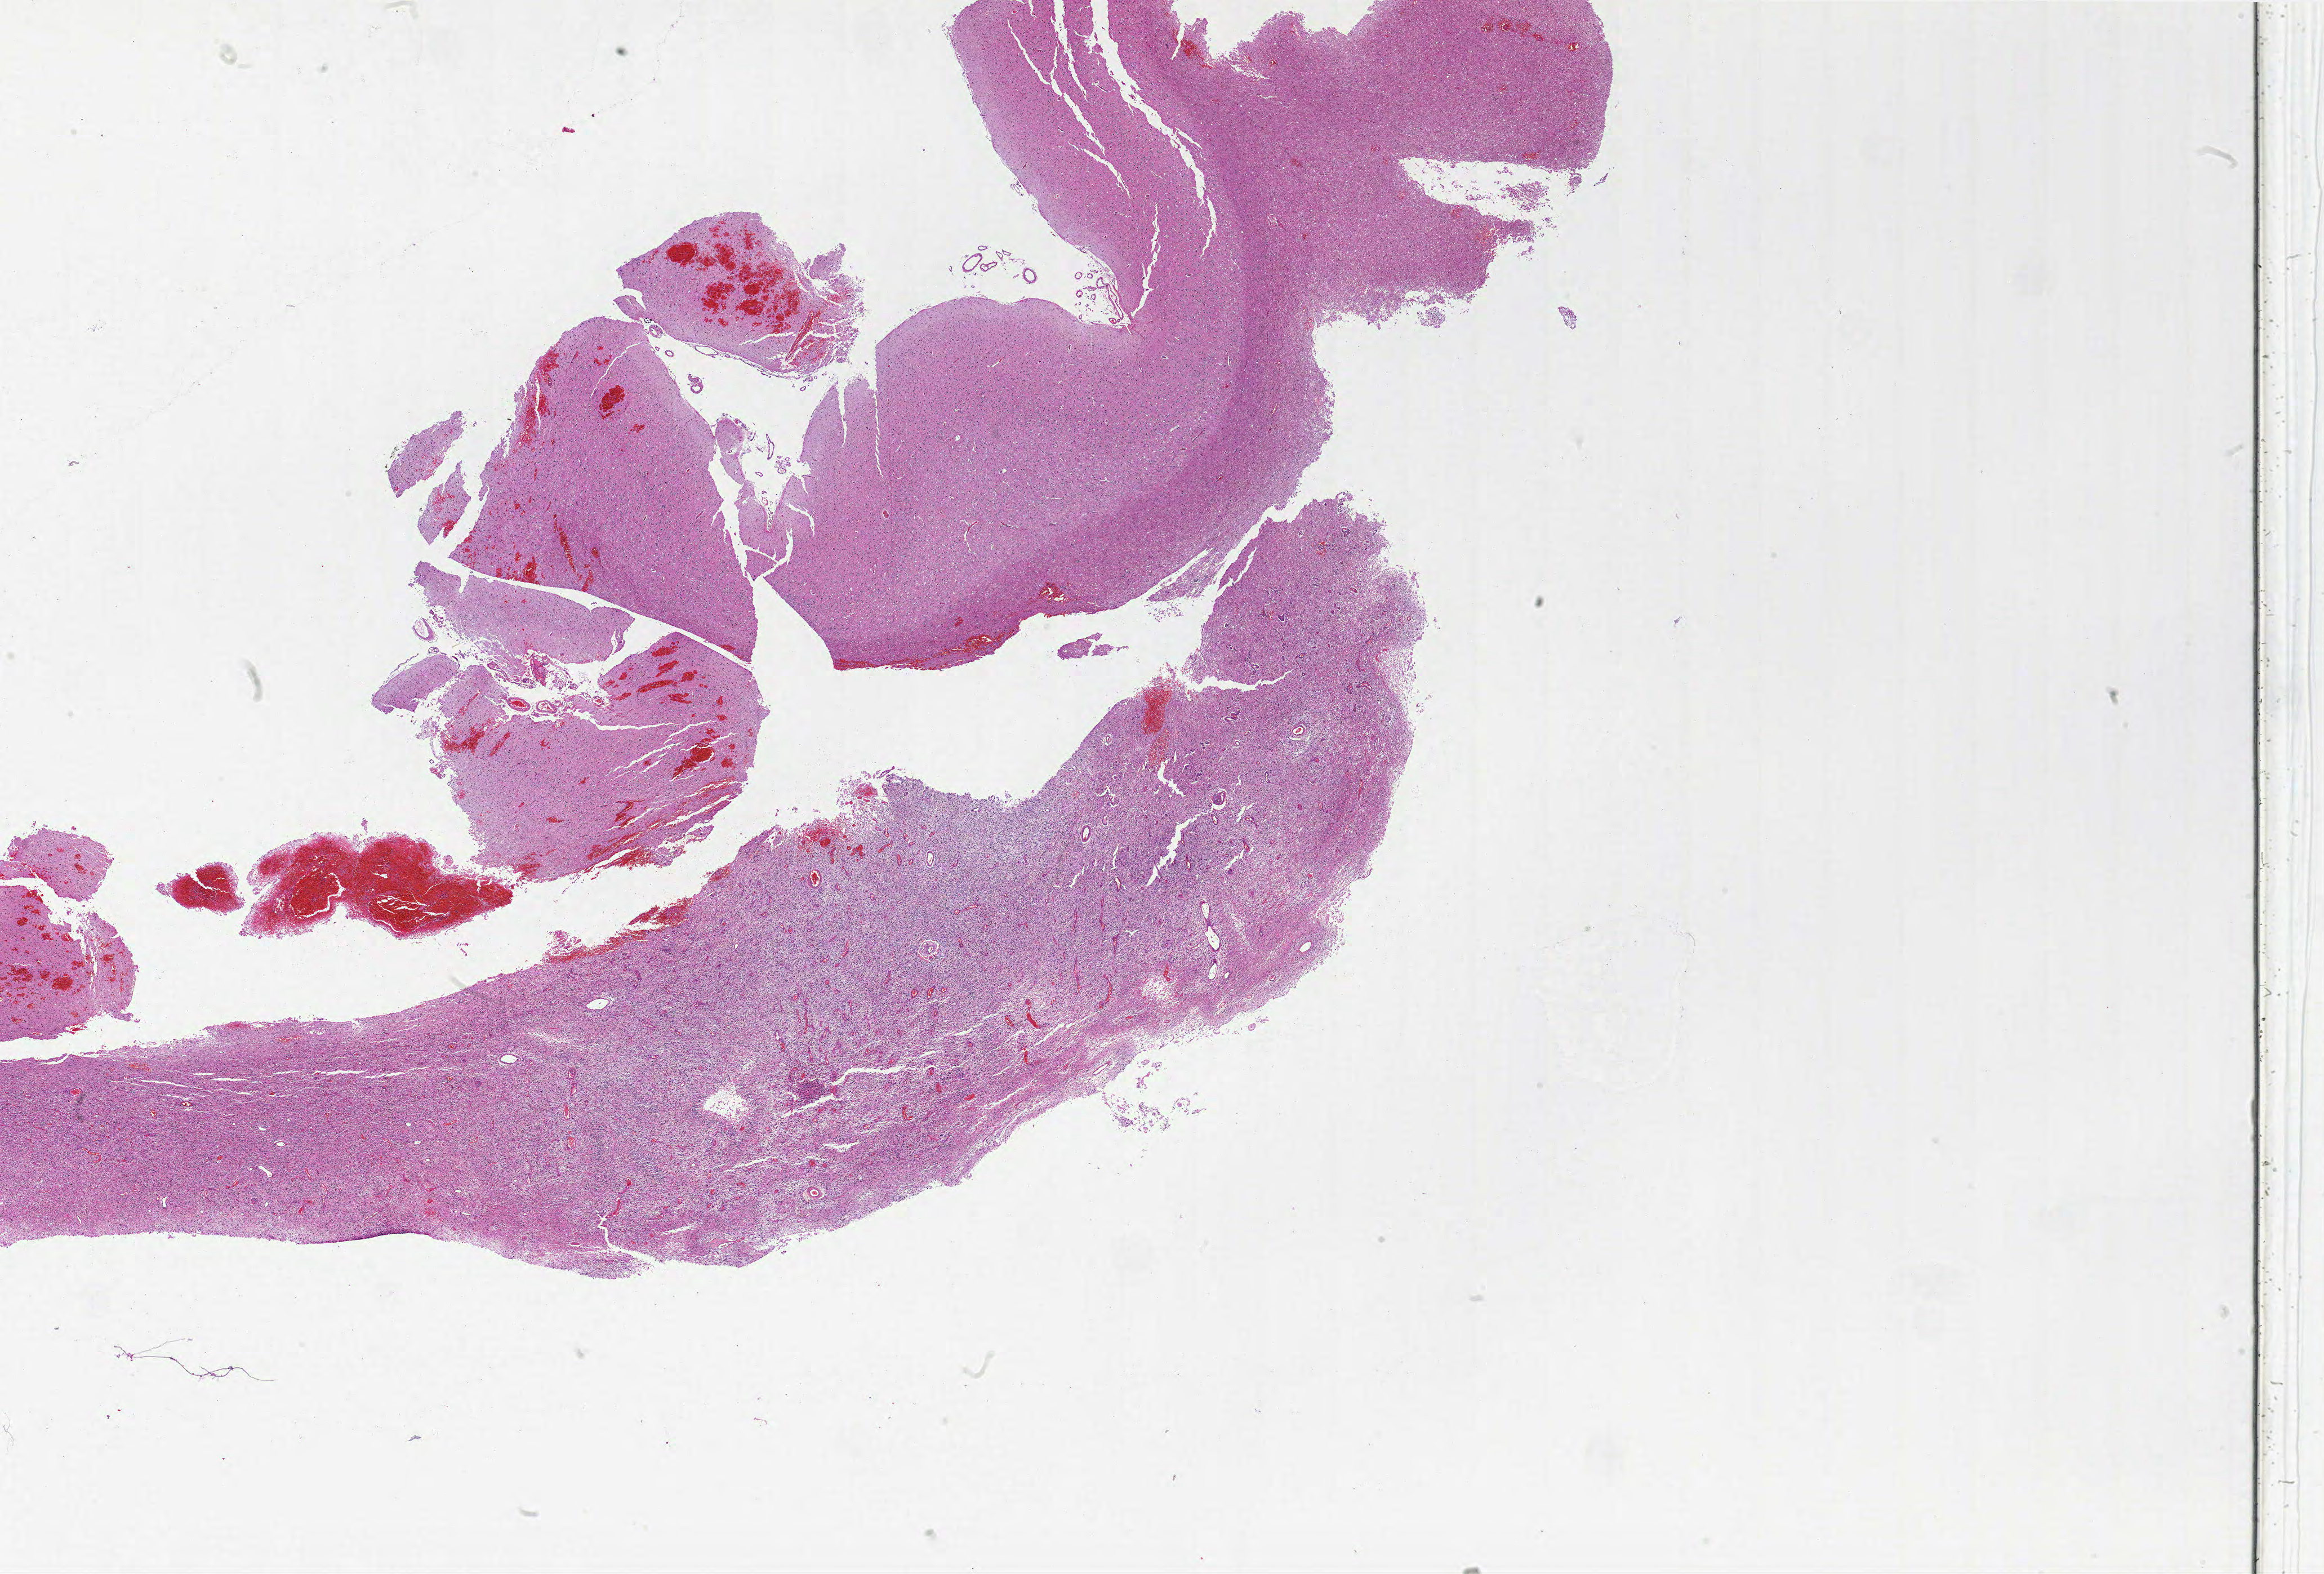
H&E whole-slide image, low-resolution overview of the scanned area, about 33.0 x 22.3 mm; formalin-fixed paraffin-embedded (FFPE) diagnostic section; sample: primary tumour, brain. Male patient; age at initial diagnosis 55 years.
Diagnosis: Glioblastoma.